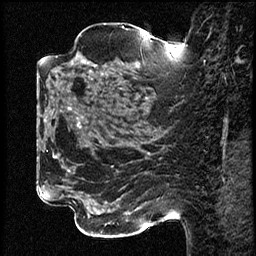
Breast MRI (dynamic contrast-enhanced), one sagittal slice; slice 31 of 78 in the series (ordered by position); dynamic contrast-enhanced study with each time point stored as its own series, time point 2 of 3 at this slice position (early post-contrast, ordered by acquisition time); 1.5 T; TE 4.2 ms, TR 17.6 ms; 2 mm slice thickness; 256 × 256 image matrix, field of view 200 × 200 mm. Female patient, age 42 years. From the clinical record (not read from this slice): setting: breast cancer imaged before/during neoadjuvant chemotherapy; receptor status: HER2-positive.
Annotated regions visible in this slice (semi-automatically segmented with operator editing):
- analysis volume of interest (the breast-tissue region the enhancement analysis was run in; not a lesion): box from (x=50, y=48) to (x=131, y=129) px
- tumour enhancement mask (voxels above the 100 % enhancement threshold inside the analysis volume of interest): (x=78, y=116)–(x=83, y=125)